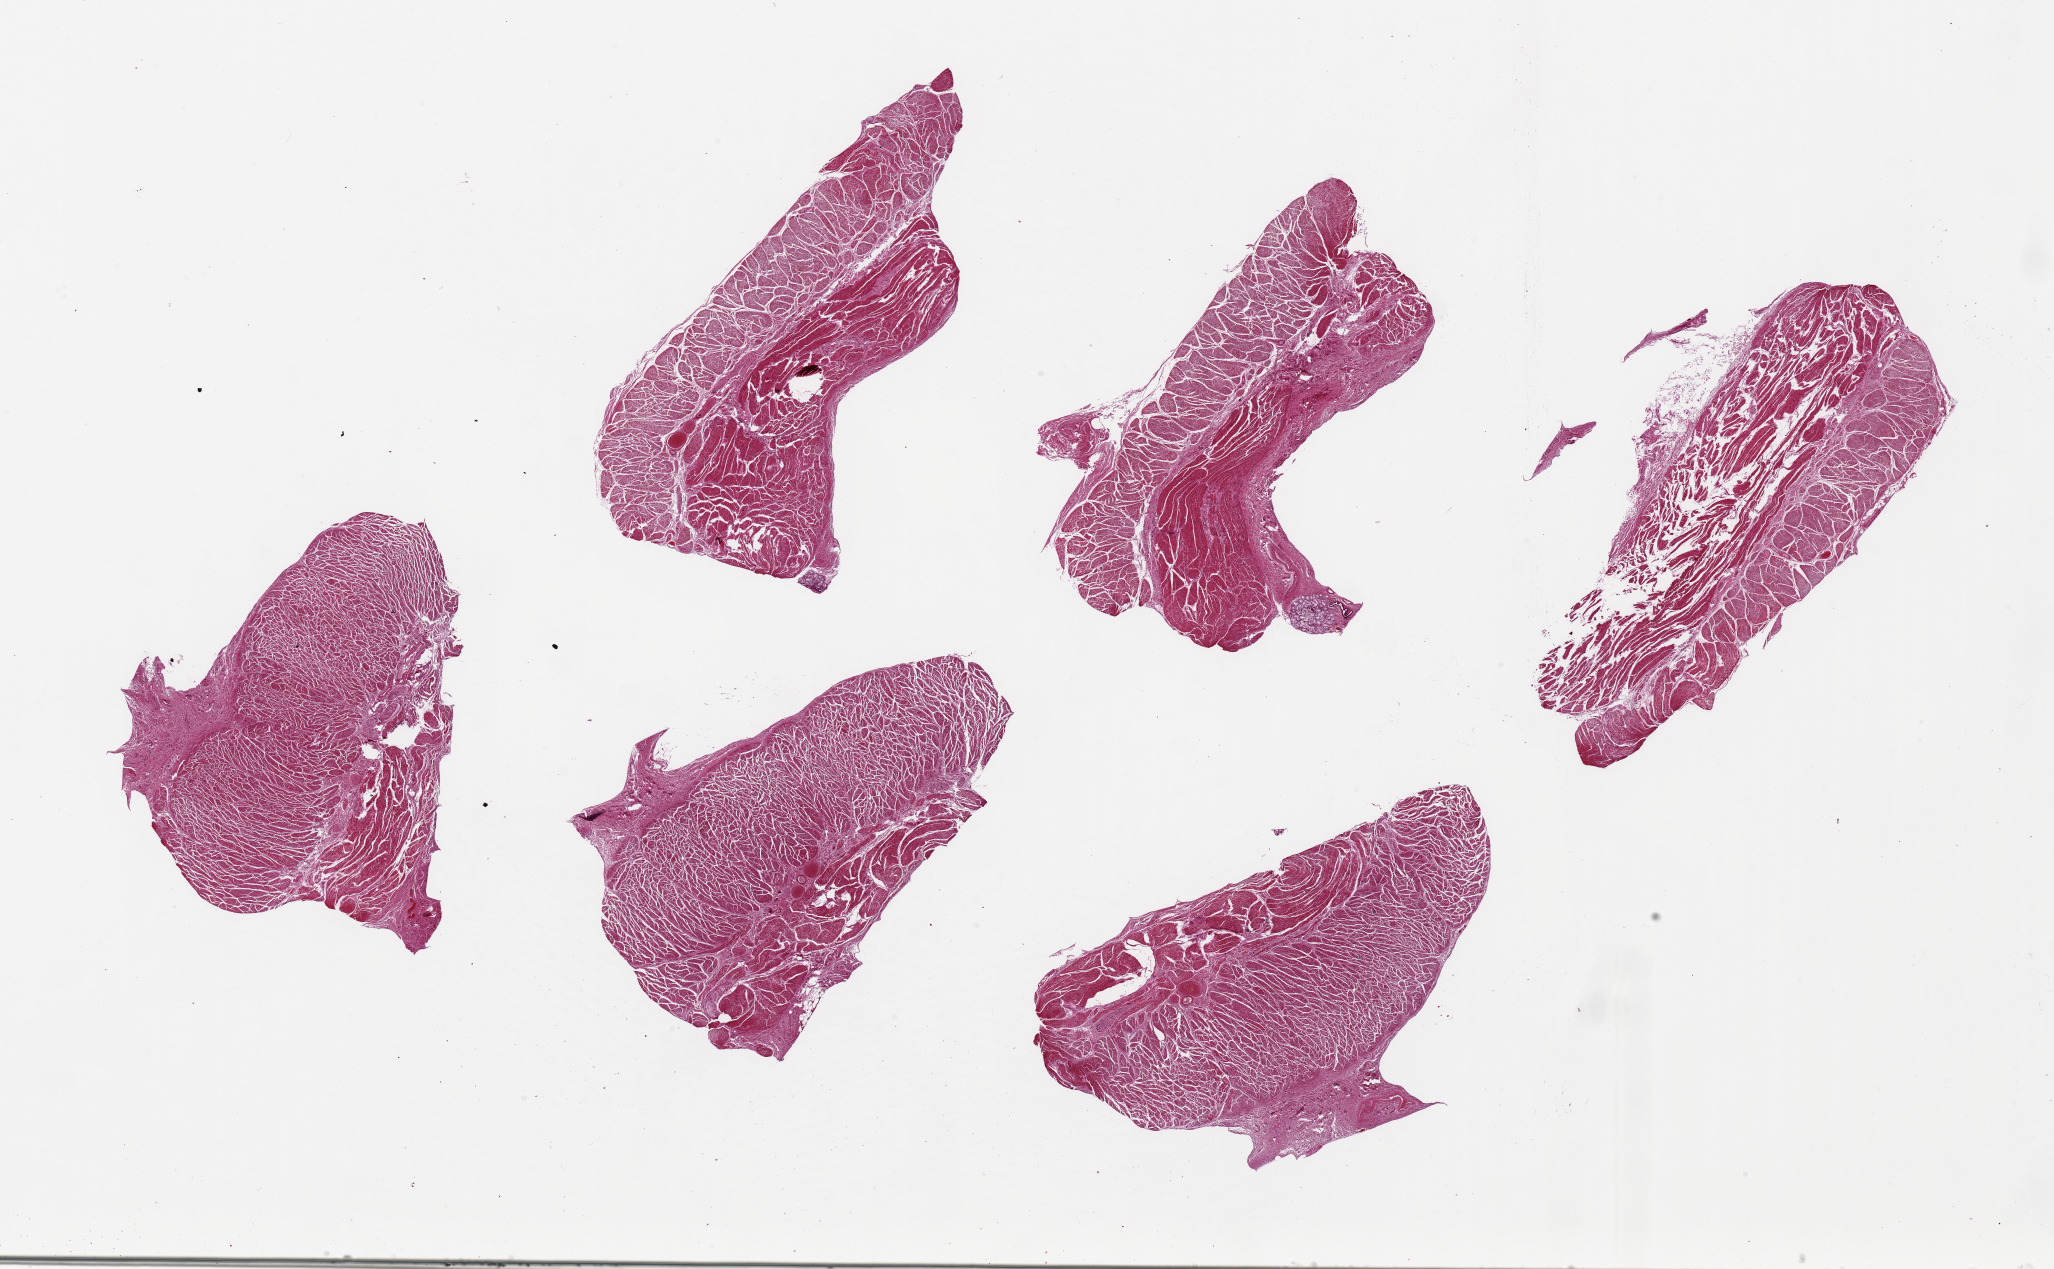
Digitized haematoxylin and eosin-stained section — shown as a low-resolution overview of the whole scanned area (about 32.5 x 20.1 mm, slide scanned at 20x); PAXgene-fixed, paraffin-embedded tissue; sampled site (target tissue): esophageal muscle; tissue donor sample. Donor sex: male.
* pathologist's review note for this sample: 6 pieces, ~8x3mm